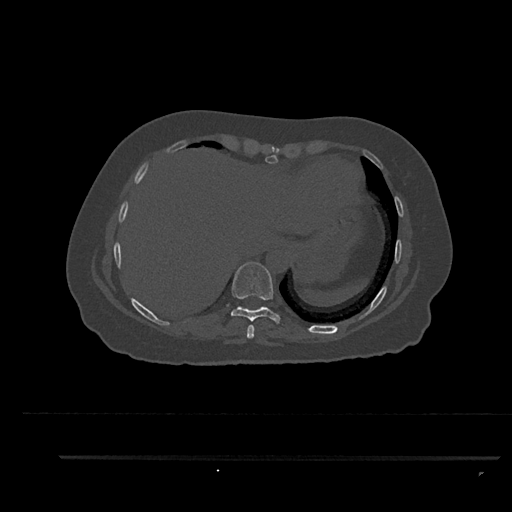
CT including the spine, one axial slice; position 413 of 797 along the scan axis; reconstruction kernel Br40s/3; 120 kVp; bone window (W 1800 / L 400 HU); 0.5 mm slice thickness; 512 × 512 image matrix, field of view 408 × 408 mm. Patient: female, 44 years. From the clinical record (not read from this slice): primary cancer: renal.
Structures marked on this image (semi-automatically segmented with operator editing):
- T8 vertebra: bounding box [x1, y1, x2, y2] px = [247, 325, 255, 339]
- T9 vertebra: [231, 262, 282, 324]